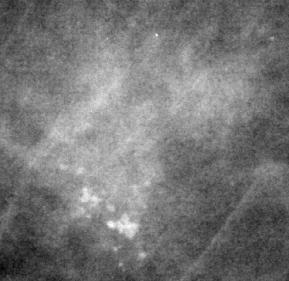
Cropped region of a digitized screen-film mammogram centred on a radiologist-marked abnormality; right breast; MLO view.
Calcifications, morphology pleomorphic, distribution clustered; BI-RADS assessment category 4; pathology result (as recorded, not read from the image): benign.